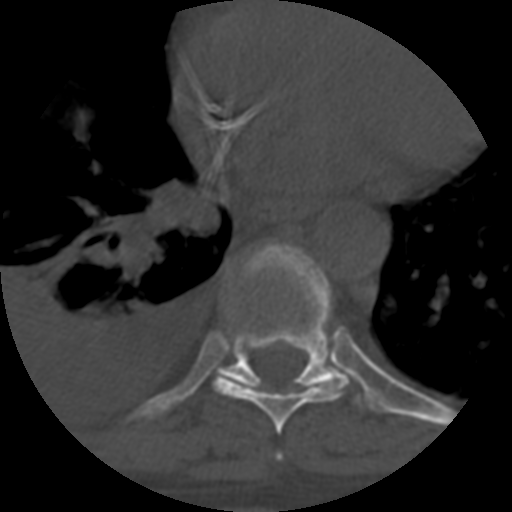
CT including the spine, one axial slice. Slice 388 of 708 in the series (ordered by position). Reconstruction kernel STANDARD. 120 kVp. One of 3 acquisitions stored at this slice position. Bone window (W 1800 / L 400 HU). 1.25 mm slice thickness. 512 × 512 image matrix. Patient age 55 years. Case-level facts recorded for this patient, not image findings: primary cancer: colon; vertebrae with lytic lesions (as recorded): T12, L1, L5.
Annotated regions visible in this slice (semi-automatically segmented with operator editing):
- T7 vertebra: bounding box [x1, y1, x2, y2] px = [278, 455, 280, 458]
- T8 vertebra: [212, 375, 349, 434]
- T9 vertebra: [217, 243, 346, 391]